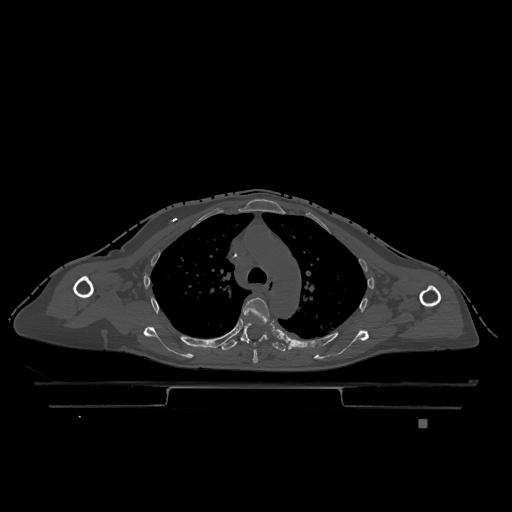
CT including the spine, one axial slice. Position 857 of 1317 along the scan axis. Bone window (W 1800 / L 400 HU). 512 × 512 image matrix, field of view 500 × 500 mm. Female patient, age 74 years. Case-level facts recorded for this patient, not image findings: primary cancer: lung; vertebrae with lytic lesions (as recorded): T1, T4, T5, T6, L4, L5.
Structures marked on this image (semi-automatically segmented with operator editing):
- T4 vertebra: bounding box <243,297,270,363> (left, top, right, bottom; pixels)
- T5 vertebra: <221,322,286,352>